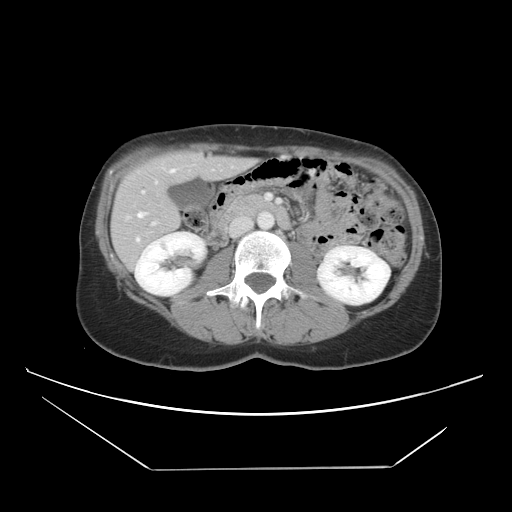
Contrast-enhanced abdominal CT, one axial slice; position 18 of 42 along the scan axis; intravenous contrast given; soft-tissue window (W 400 / L 40 HU); 5 mm slice thickness; 512 × 512 image matrix, field of view 399 × 399 mm. Female patient, age 52 years. Case-level facts recorded for this patient, not image findings: diagnosis: colorectal cancer liver metastases, imaged before liver resection; multiple liver metastases: yes; largest metastasis: 5.5 cm; disease in both lobes: yes.
Structures marked on this image (outlined manually by an expert reader):
- hepatic veins: bounding box <126,162,195,243> (left, top, right, bottom; pixels)
- liver: <112,153,250,266>
- planned liver remnant (the part of the liver to remain after resection): <118,153,213,211>
- portal vein (with intrahepatic branches): <142,164,270,226>